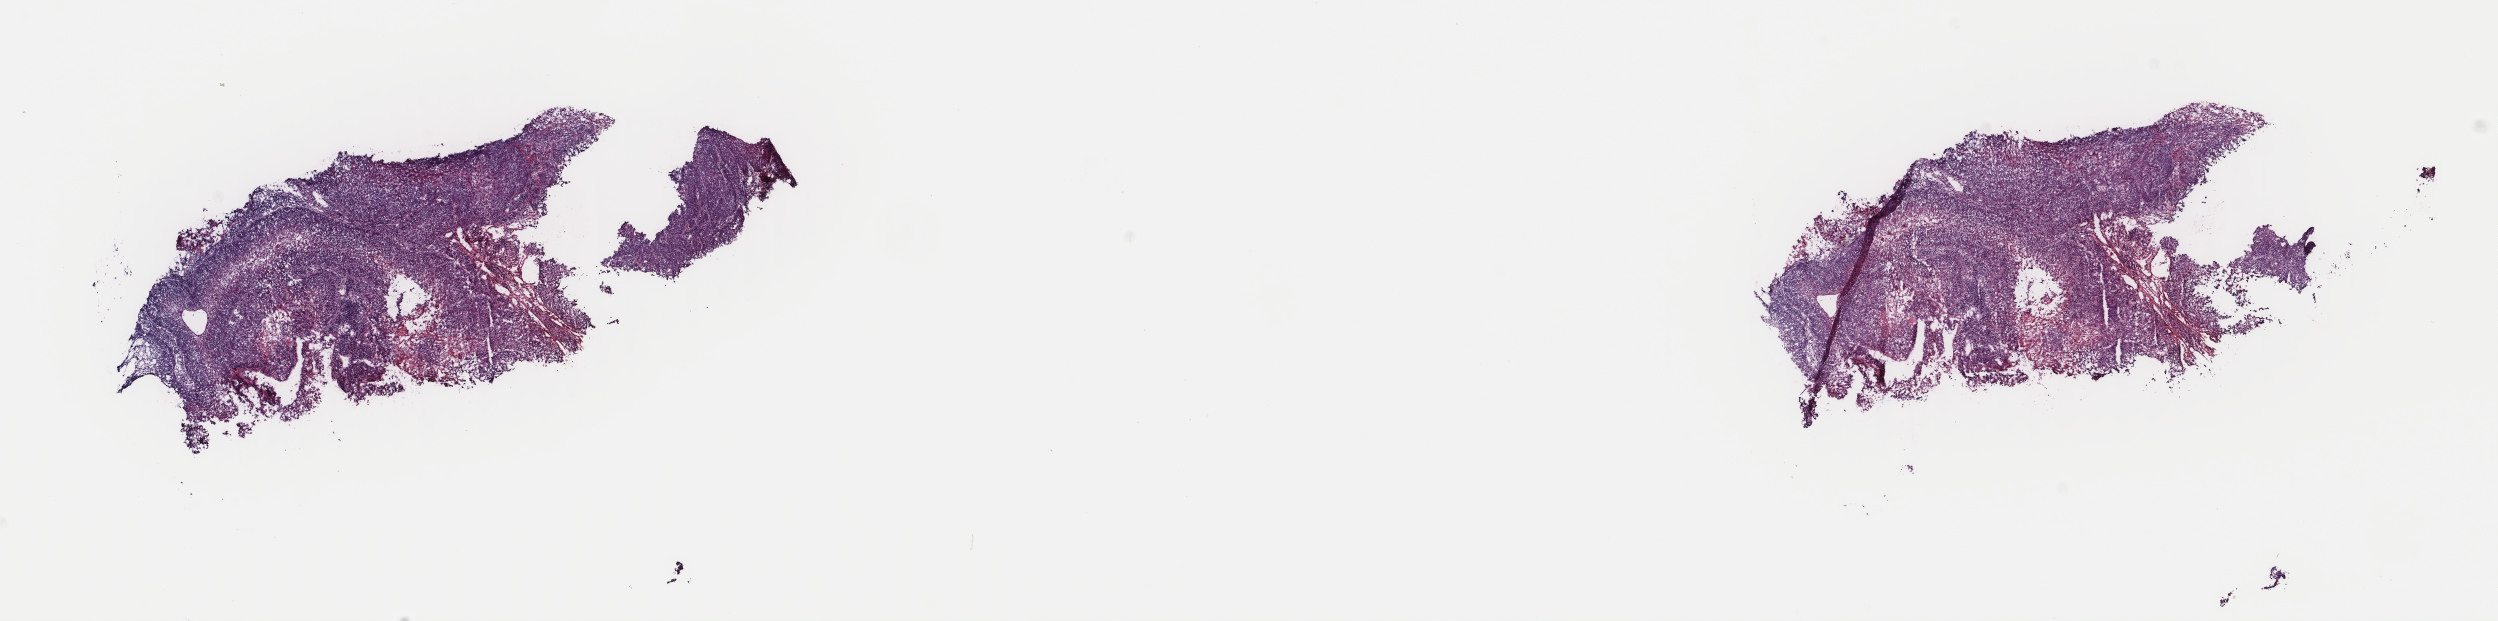
Digitized Hematoxylin and eosin (H&E) stained tissue section (whole slide), low-resolution overview of the scanned area, about 19.8 x 4.9 mm. Frozen section from the top of the tissue portion. Sample: primary tumour, head and neck. Female, age 73 years at initial diagnosis. Histologic grade: G1 (well differentiated). Pathologist review of this section (percent, as recorded): tumour cells 97%, tumour nuclei 75%, normal cells 0%, stromal cells 0%, necrosis 3%. Infiltration values recorded for this section: lymphocyte infiltration 3%, monocyte infiltration 0%, neutrophil infiltration 0%.
Pathologic diagnosis: Squamous cell carcinoma, keratinizing, NOS (floor of mouth, NOS).